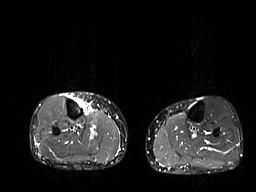
MRI of an extremity soft-tissue mass, one axial slice; position 11 of 32 along the scan axis; STIR; 6 mm slice thickness; 256 × 192 image matrix, field of view 375 × 281 mm. Female patient. Case-level facts recorded for this patient, not image findings: histological type: undifferentiated – high grade; grade: high; site of the primary tumour: right thigh.
Outlined on this slice (manually delineated by an expert):
- gross tumour volume (mass): bounding box (x1, y1, x2, y2) in pixels: (71, 98, 88, 112)